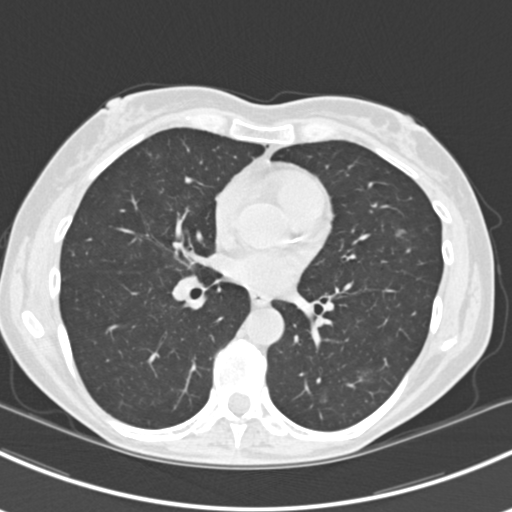
Low-dose screening chest CT, axial slice; first (baseline) screen; lung window (W 1500 / L -600 HU); 2 mm slice thickness; standard (soft-tissue) reconstruction kernel (B30f). Female, age 63 years at enrolment. Current smoker at enrolment.
• Expert reader's lesion annotation, box from (x=380, y=218) to (x=423, y=257) px.
• The screening reader recorded 10 non-calcified nodules or masses ≥4 mm on this exam; which of them this box marks is not recorded.